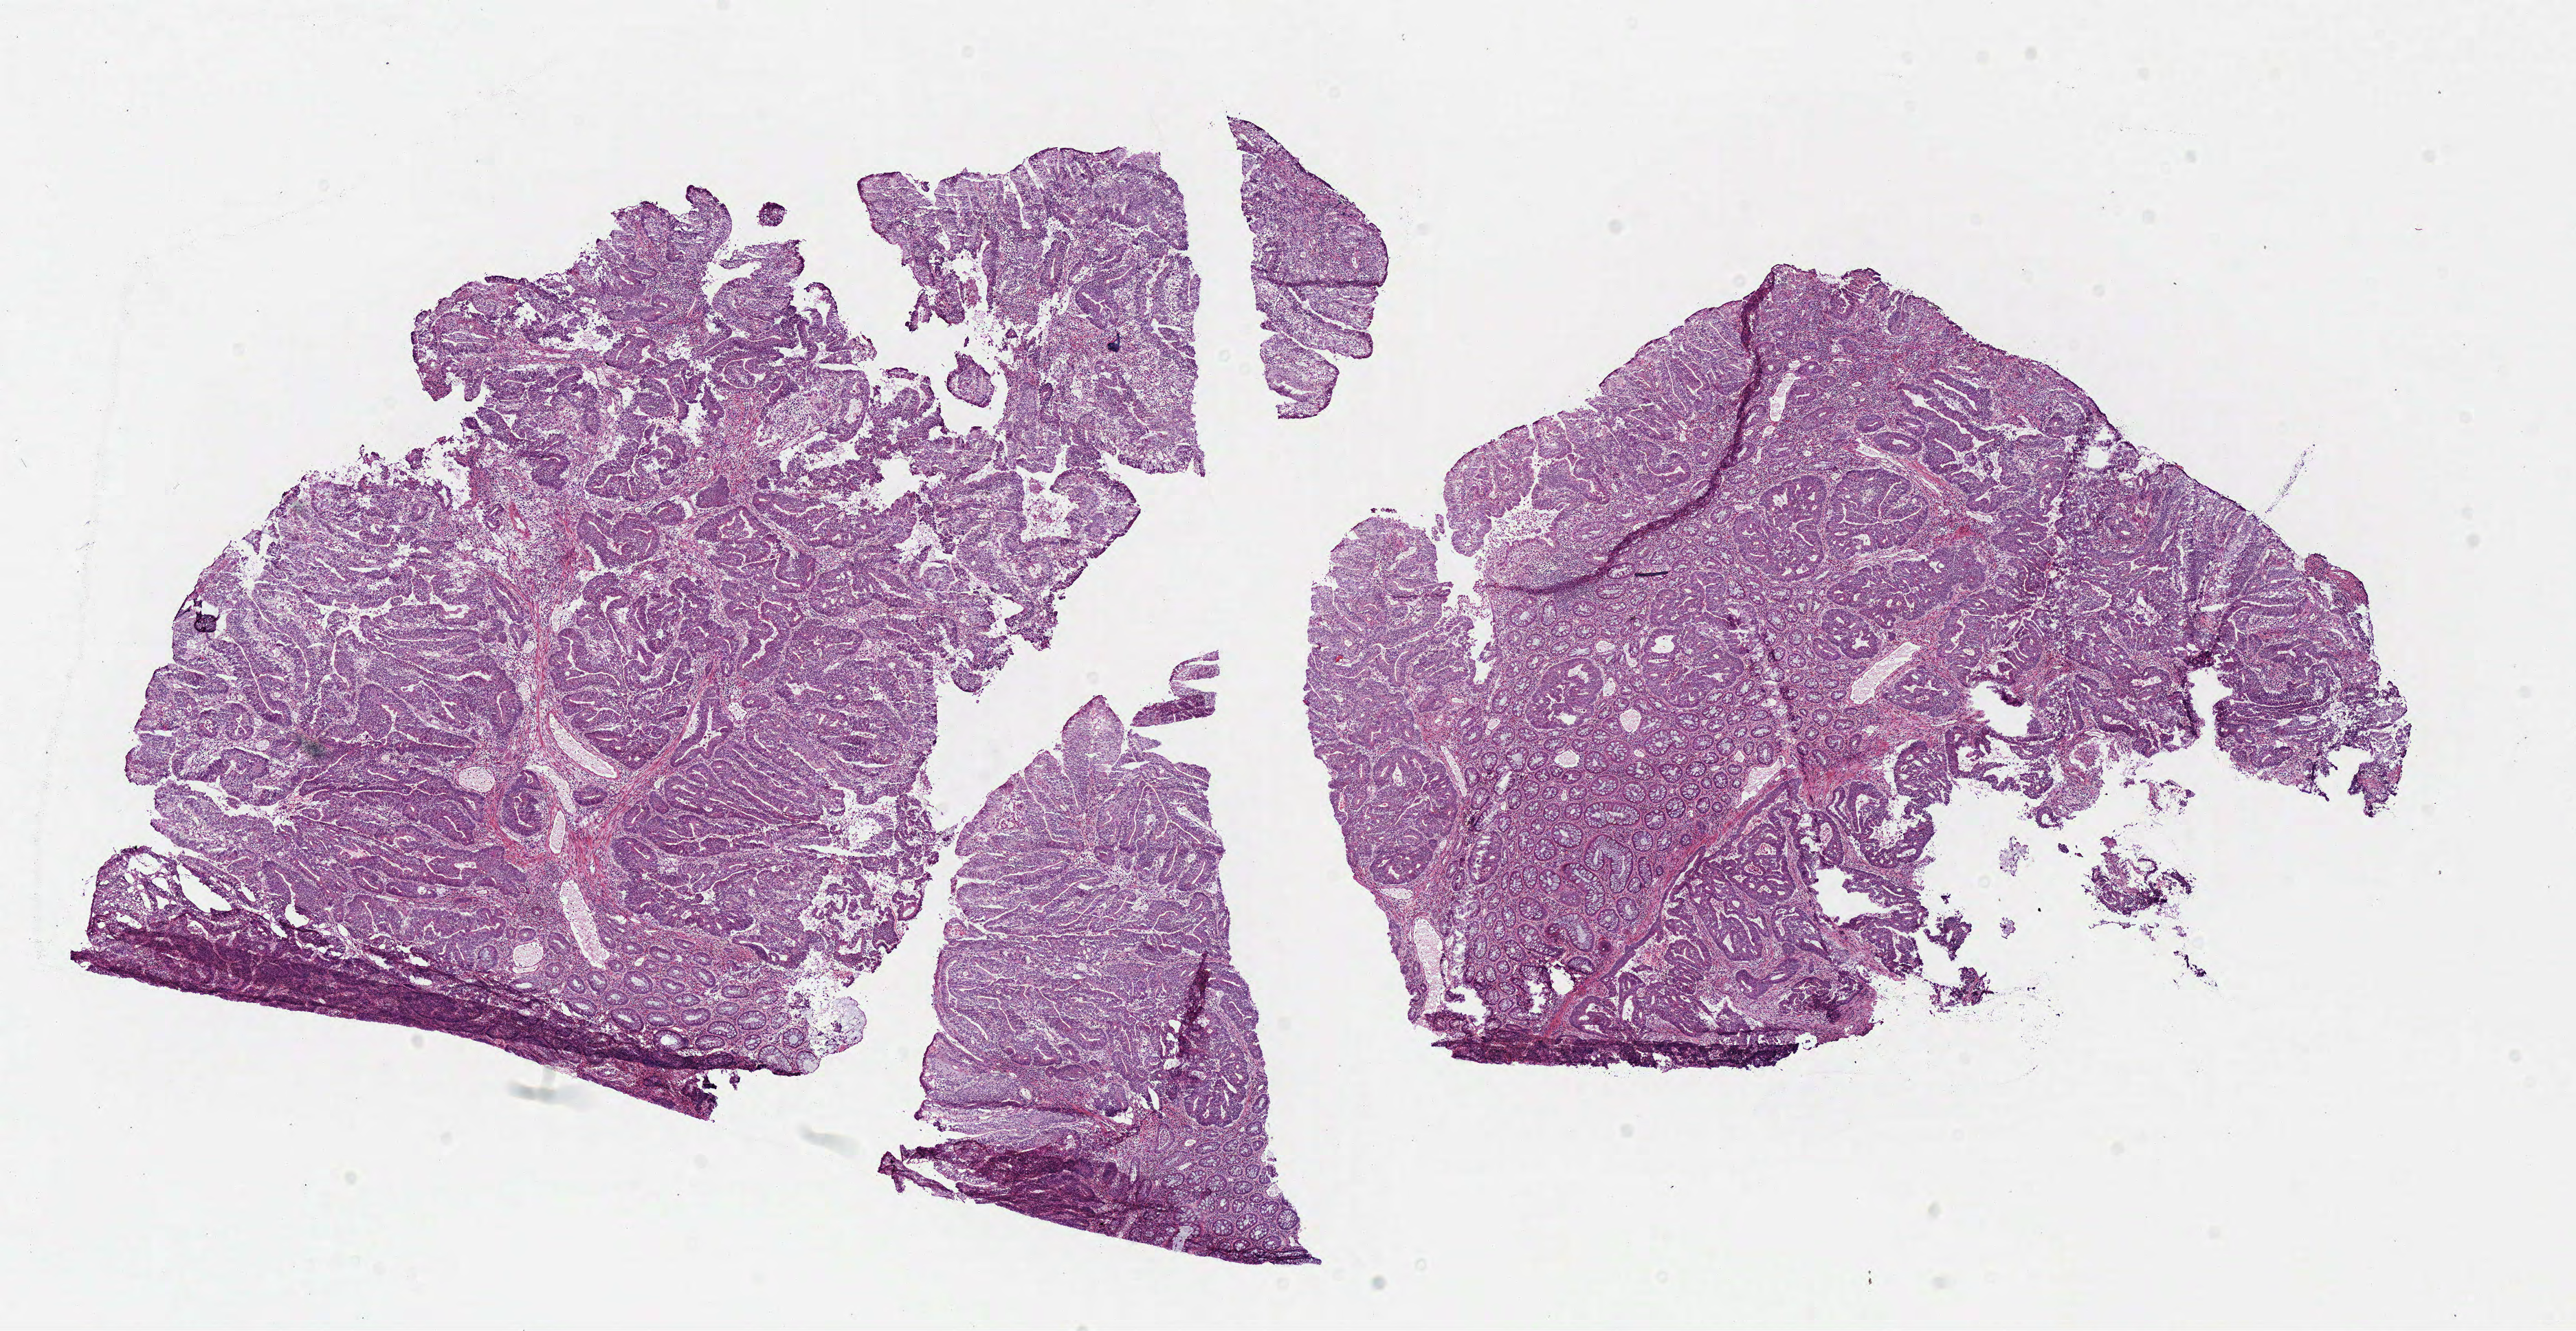
Whole-slide histology image, Hematoxylin and eosin (H&E) stained — a low-resolution overview of the entire scanned area, about 14.8 x 7.6 mm (from a 40x scan). Frozen section. Sample: primary tumour, rectum. Patient: male, age at initial diagnosis 68 years. Pathologist review of this section (percent, as recorded): tumour cells 72%, tumour nuclei 70%, normal cells 10%, stromal cells 10%, necrosis 8%.
TNM: T2 N0 M0. AJCC pathologic stage: I (6th edition). Lymph nodes positive (case pathology): 0 of 8 examined. Pathologic diagnosis: Adenocarcinoma, NOS (rectosigmoid junction).